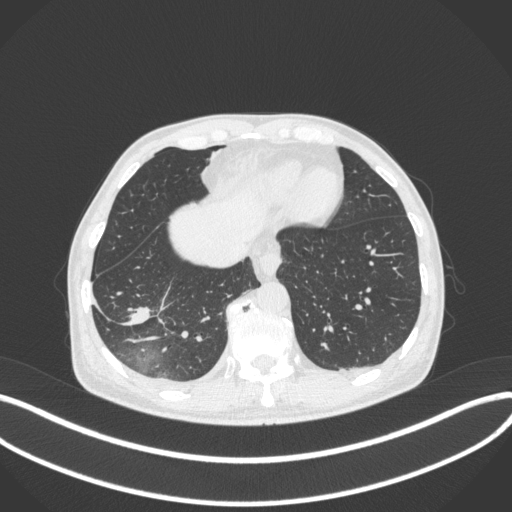
Chest CT, one axial slice; slice 90 of 385 in the series (ordered by position); reconstruction kernel B31f; lung window (W 1500 / L -600 HU); 1 mm slice thickness; 512 × 512 image matrix, field of view 400 × 400 mm. Patient: male, 64 years. From the clinical record (not read from this slice): clinical TNM (as recorded): T3 N0 M0; histopathological grade: G2-3.
Outlined on this slice (bounding box drawn by a radiologist):
- lung tumour (recorded histology: adenocarcinoma): box from (x=122, y=307) to (x=155, y=328) px